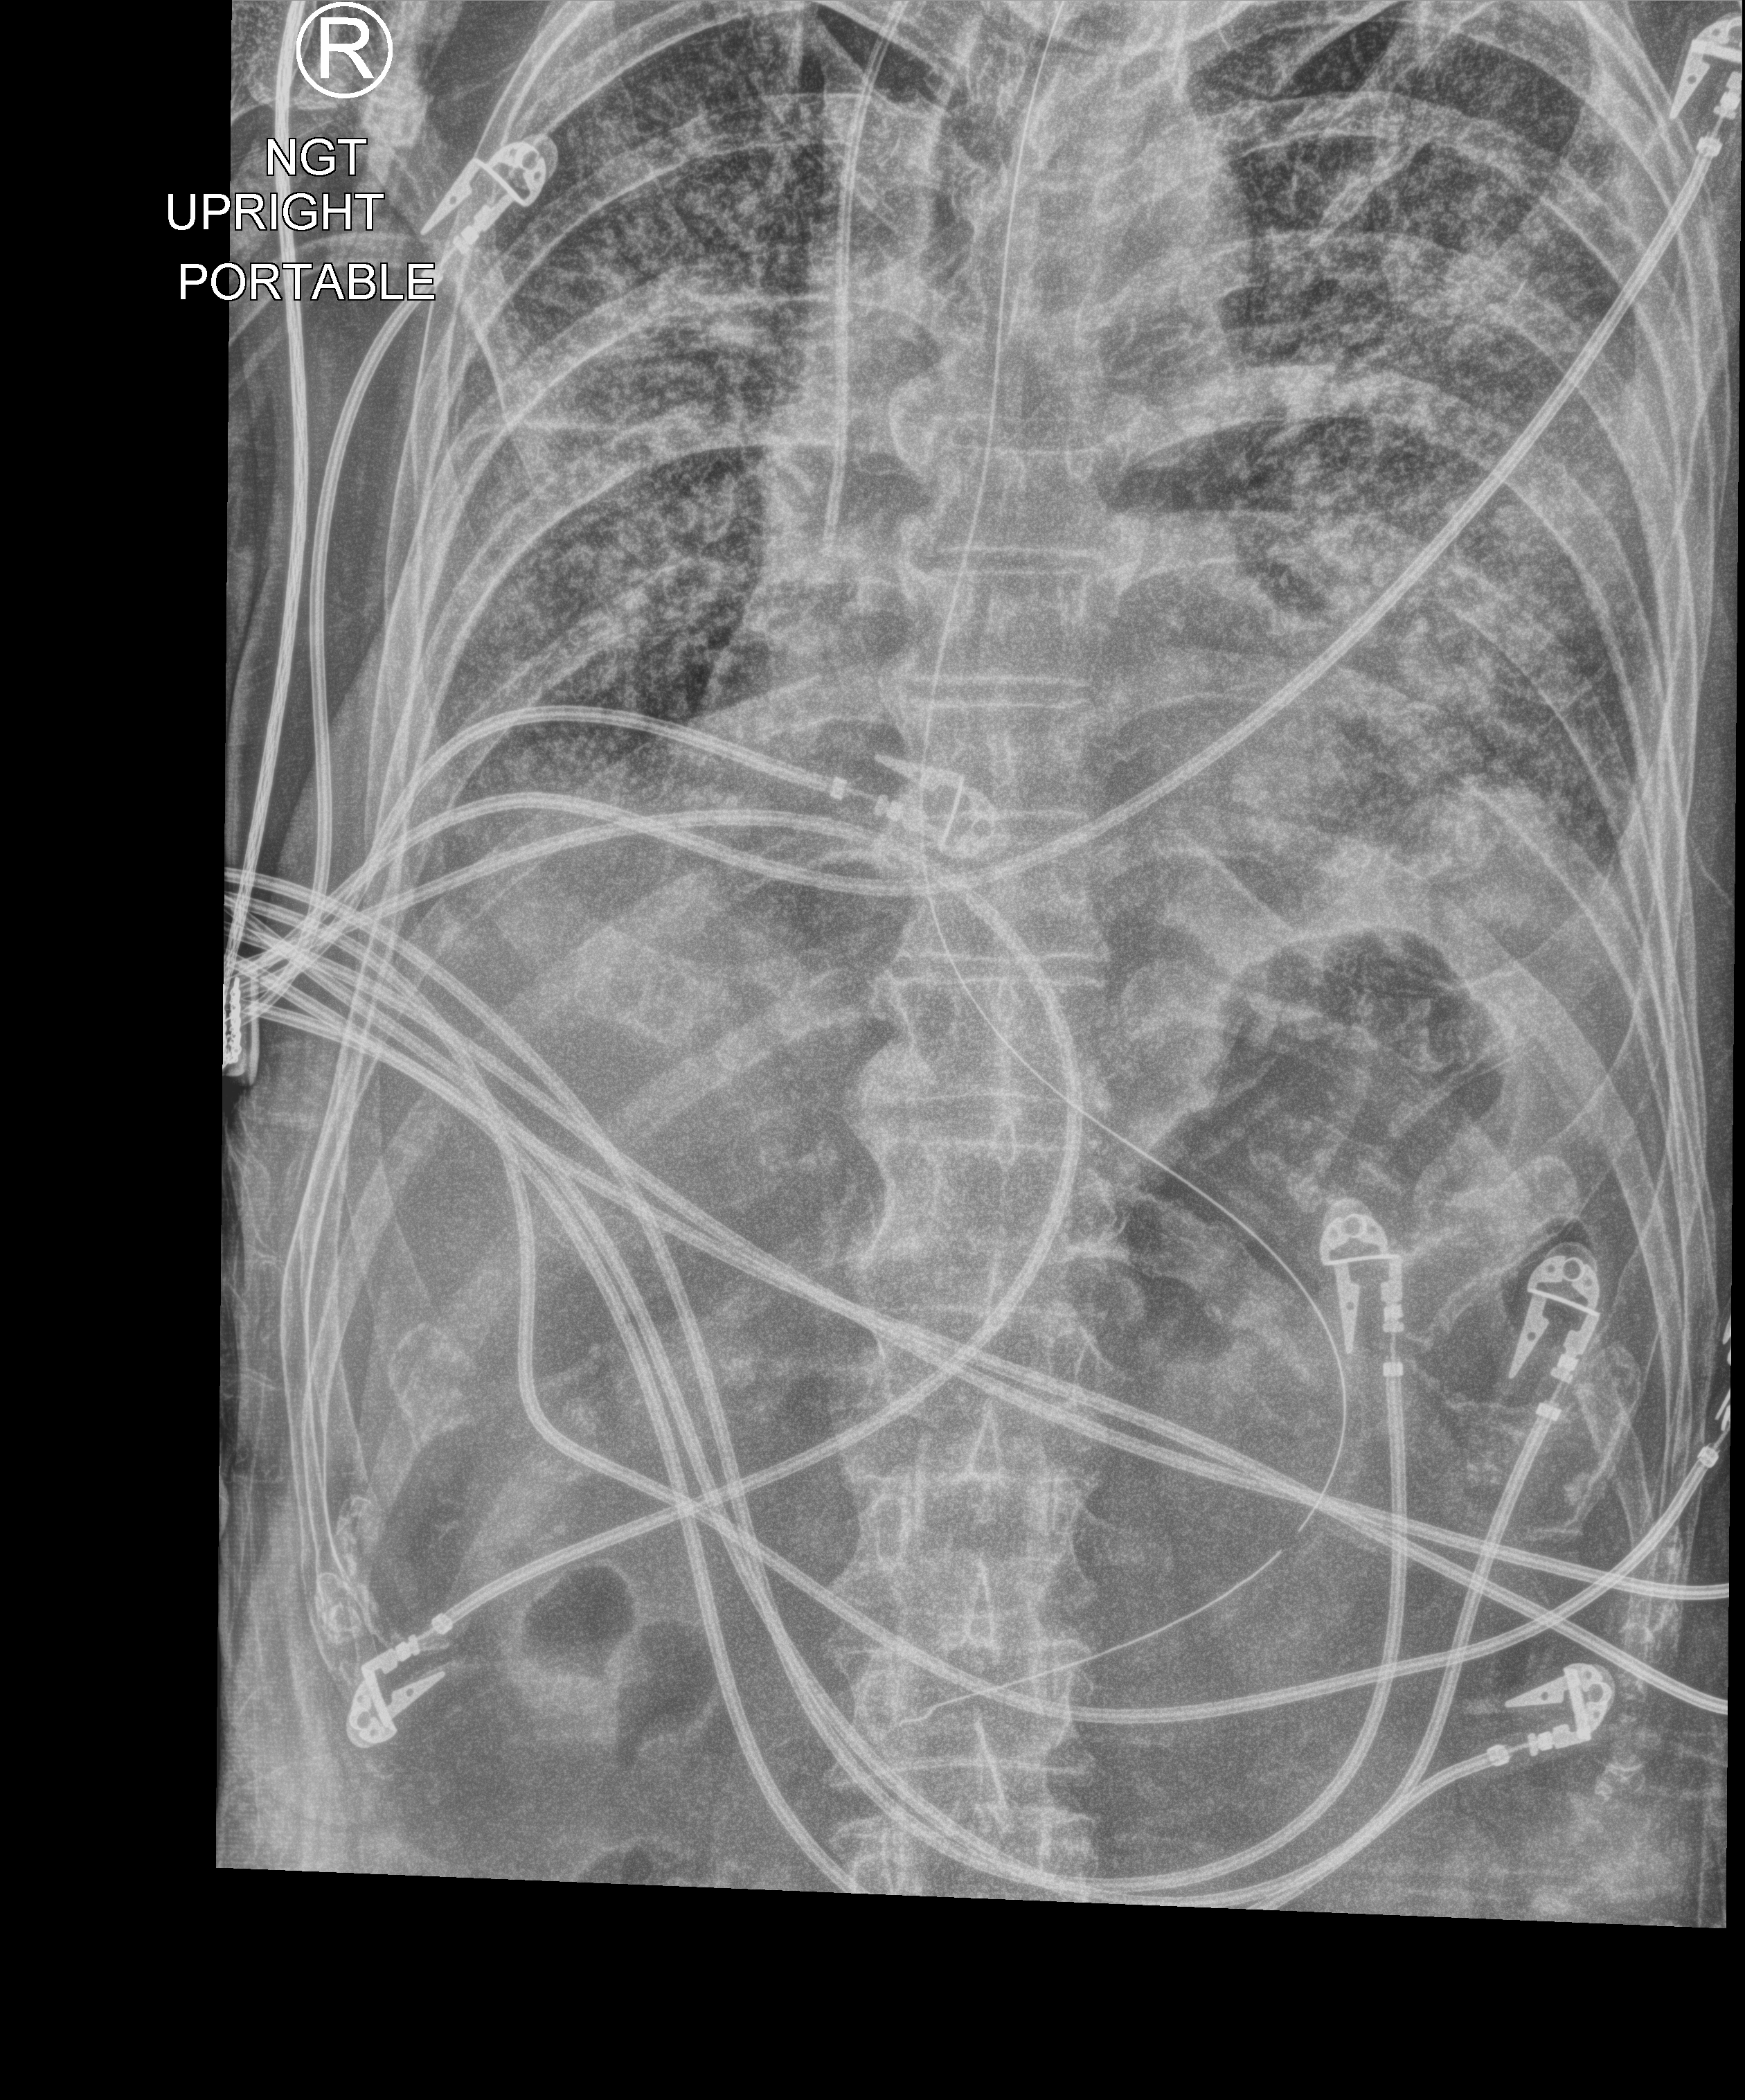
Portable chest radiograph; anteroposterior (AP) projection. Male patient hospitalised with COVID-19, age 60–74 years.
Admission-level facts for this patient (not findings on this image; timing relative to this image not recorded): mechanically ventilated during this hospital stay: yes.